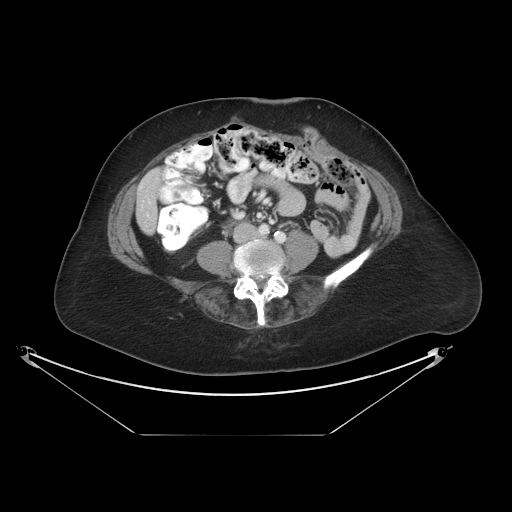
Contrast-enhanced abdominal CT, one axial slice. Slice 2 of 36 in the series (ordered by position). Reconstruction kernel STANDARD. 120 kVp. Intravenous contrast given. Soft-tissue window (W 400 / L 40 HU). 512 × 512 image matrix, field of view 500 × 500 mm. Female patient, age 70 years. Case-level facts recorded for this patient, not image findings: diagnosis: colorectal cancer liver metastases, imaged before liver resection; multiple liver metastases: no; largest metastasis: 2.5 cm.
Annotated regions visible in this slice (expert manual segmentation):
- liver: bounding box [x1, y1, x2, y2] px = [137, 172, 160, 234]